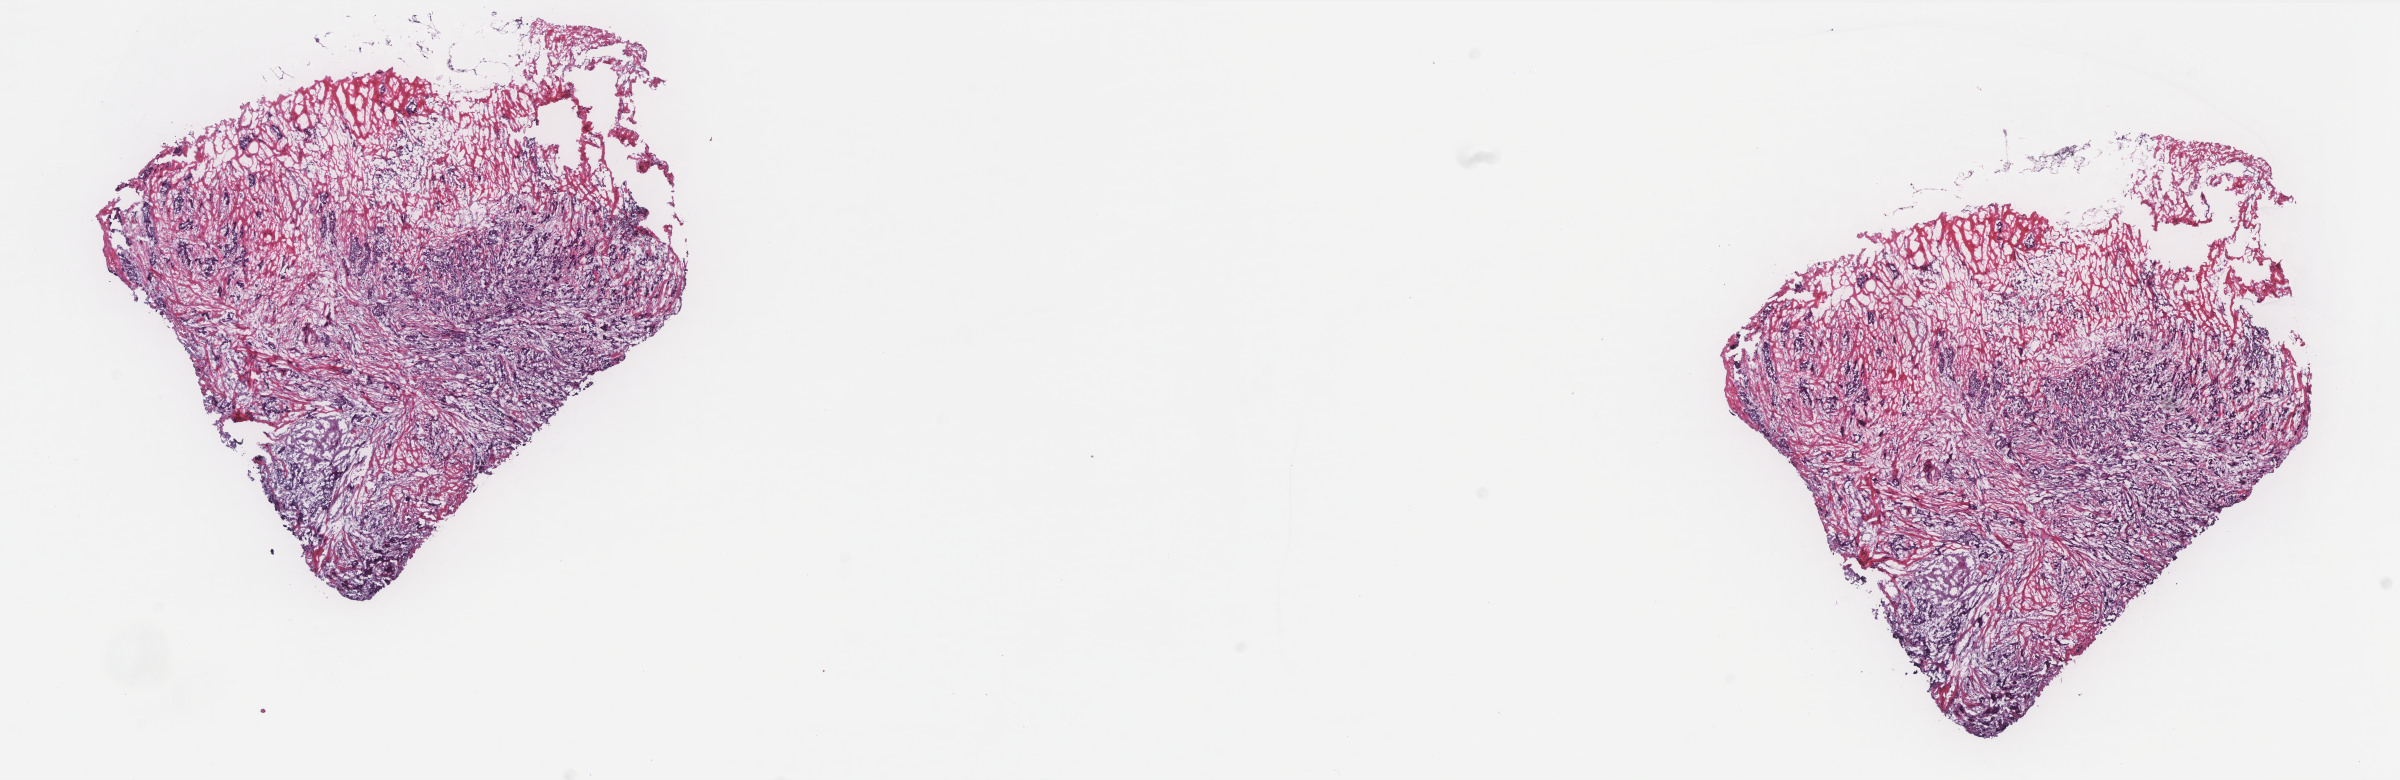
Digitized Hematoxylin and eosin (H&E) stained tissue section (whole slide) — low-resolution overview of the scanned area, about 19.2 x 6.3 mm (acquisition: 40x scan), frozen section from the top of the tissue portion, breast, primary tumour sample. Patient: female, age at initial diagnosis 56 years. Pathologist review of this section (percent, as recorded): tumour cells 60%, tumour nuclei 60%, normal cells 2%, stromal cells 38%, necrosis 0%. Infiltration values recorded for this section: lymphocyte infiltration 5%, monocyte infiltration 1%, neutrophil infiltration 1%.
• AJCC pathologic stage: IA (7th edition)
• laterality: right
• pathologic diagnosis: Infiltrating duct carcinoma, NOS